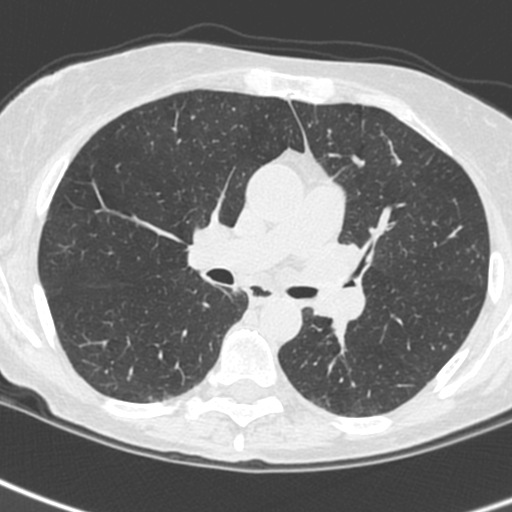
Low-dose screening chest CT, one axial slice; position 146 of 242 along the scan axis; lung window (W 1500 / L -600 HU); 1.3 mm slice thickness; 512 × 512 image matrix, field of view 284 × 284 mm.
Outlined on this slice (expert manual segmentation):
- lesion 3 (tumor, upper lobe of left lung): bounding box (x1, y1, x2, y2) in pixels: (305, 240, 366, 327)